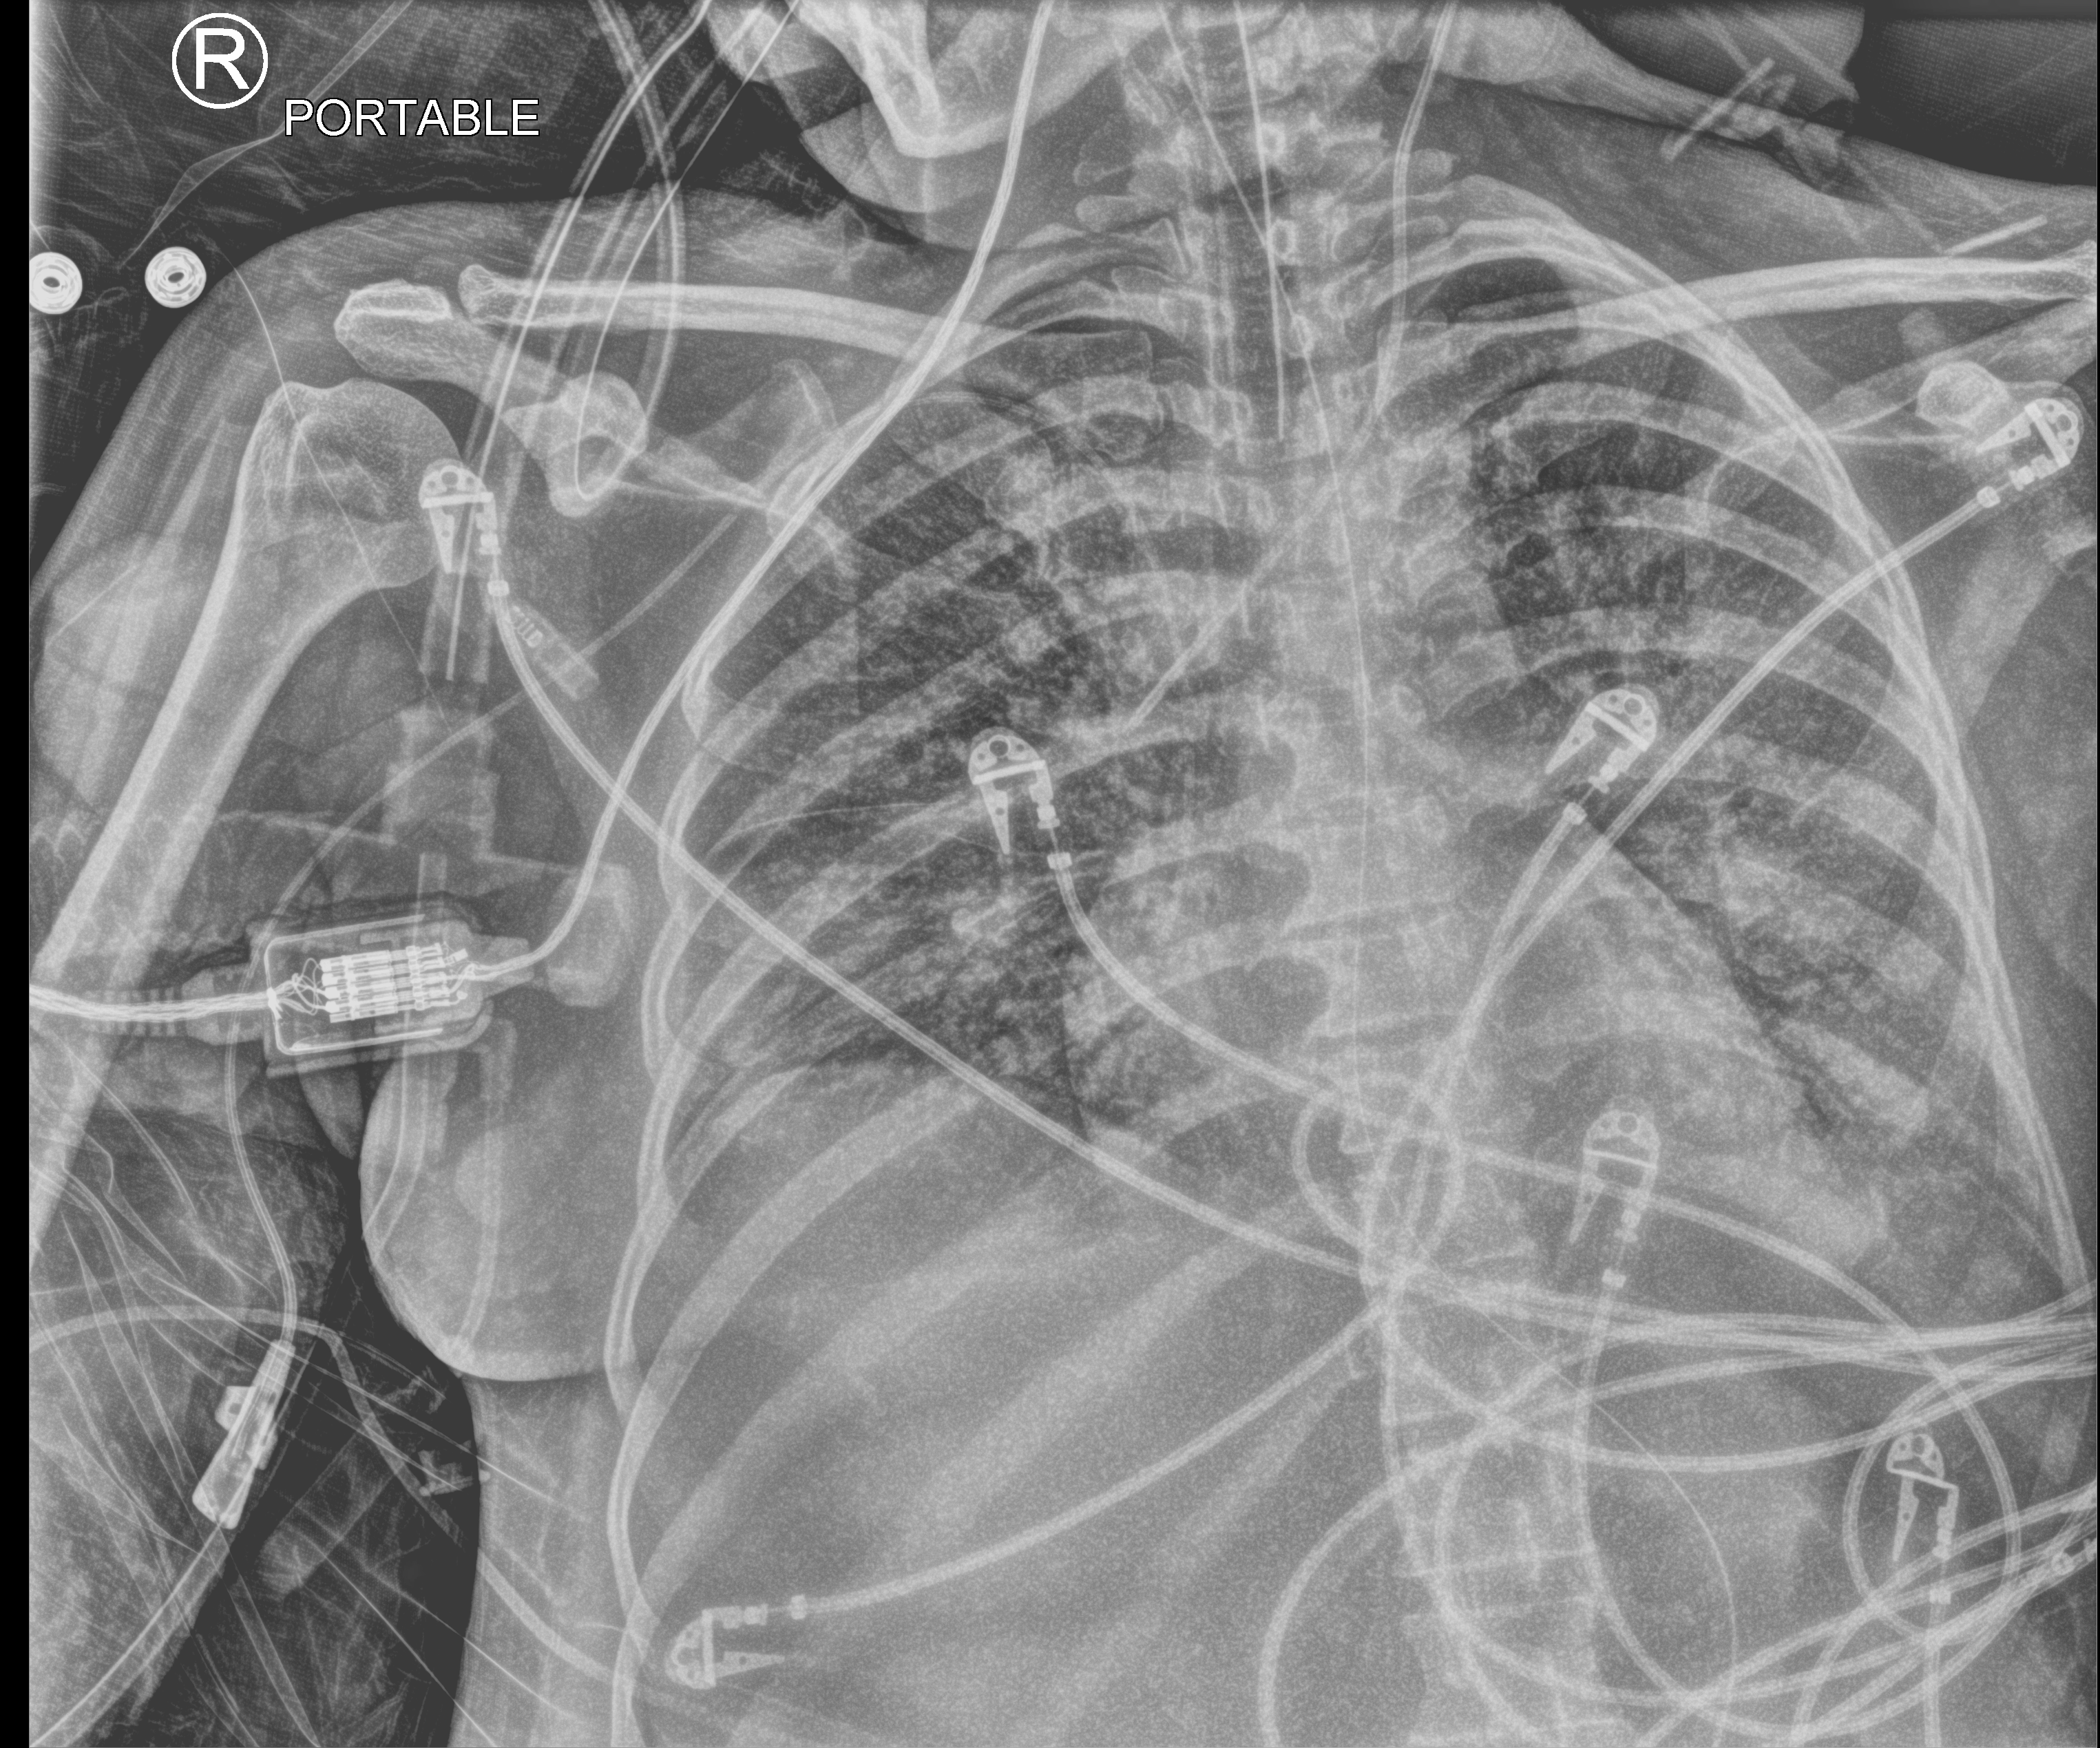
Chest X-ray (portable); anteroposterior (AP) projection. Female patient hospitalised with COVID-19, age 18–59 years.
Hospital-stay facts (about this admission, not read from this image; timing relative to this image not recorded): admitted to intensive care during this hospital stay: yes; chronic kidney disease (admission record): no.